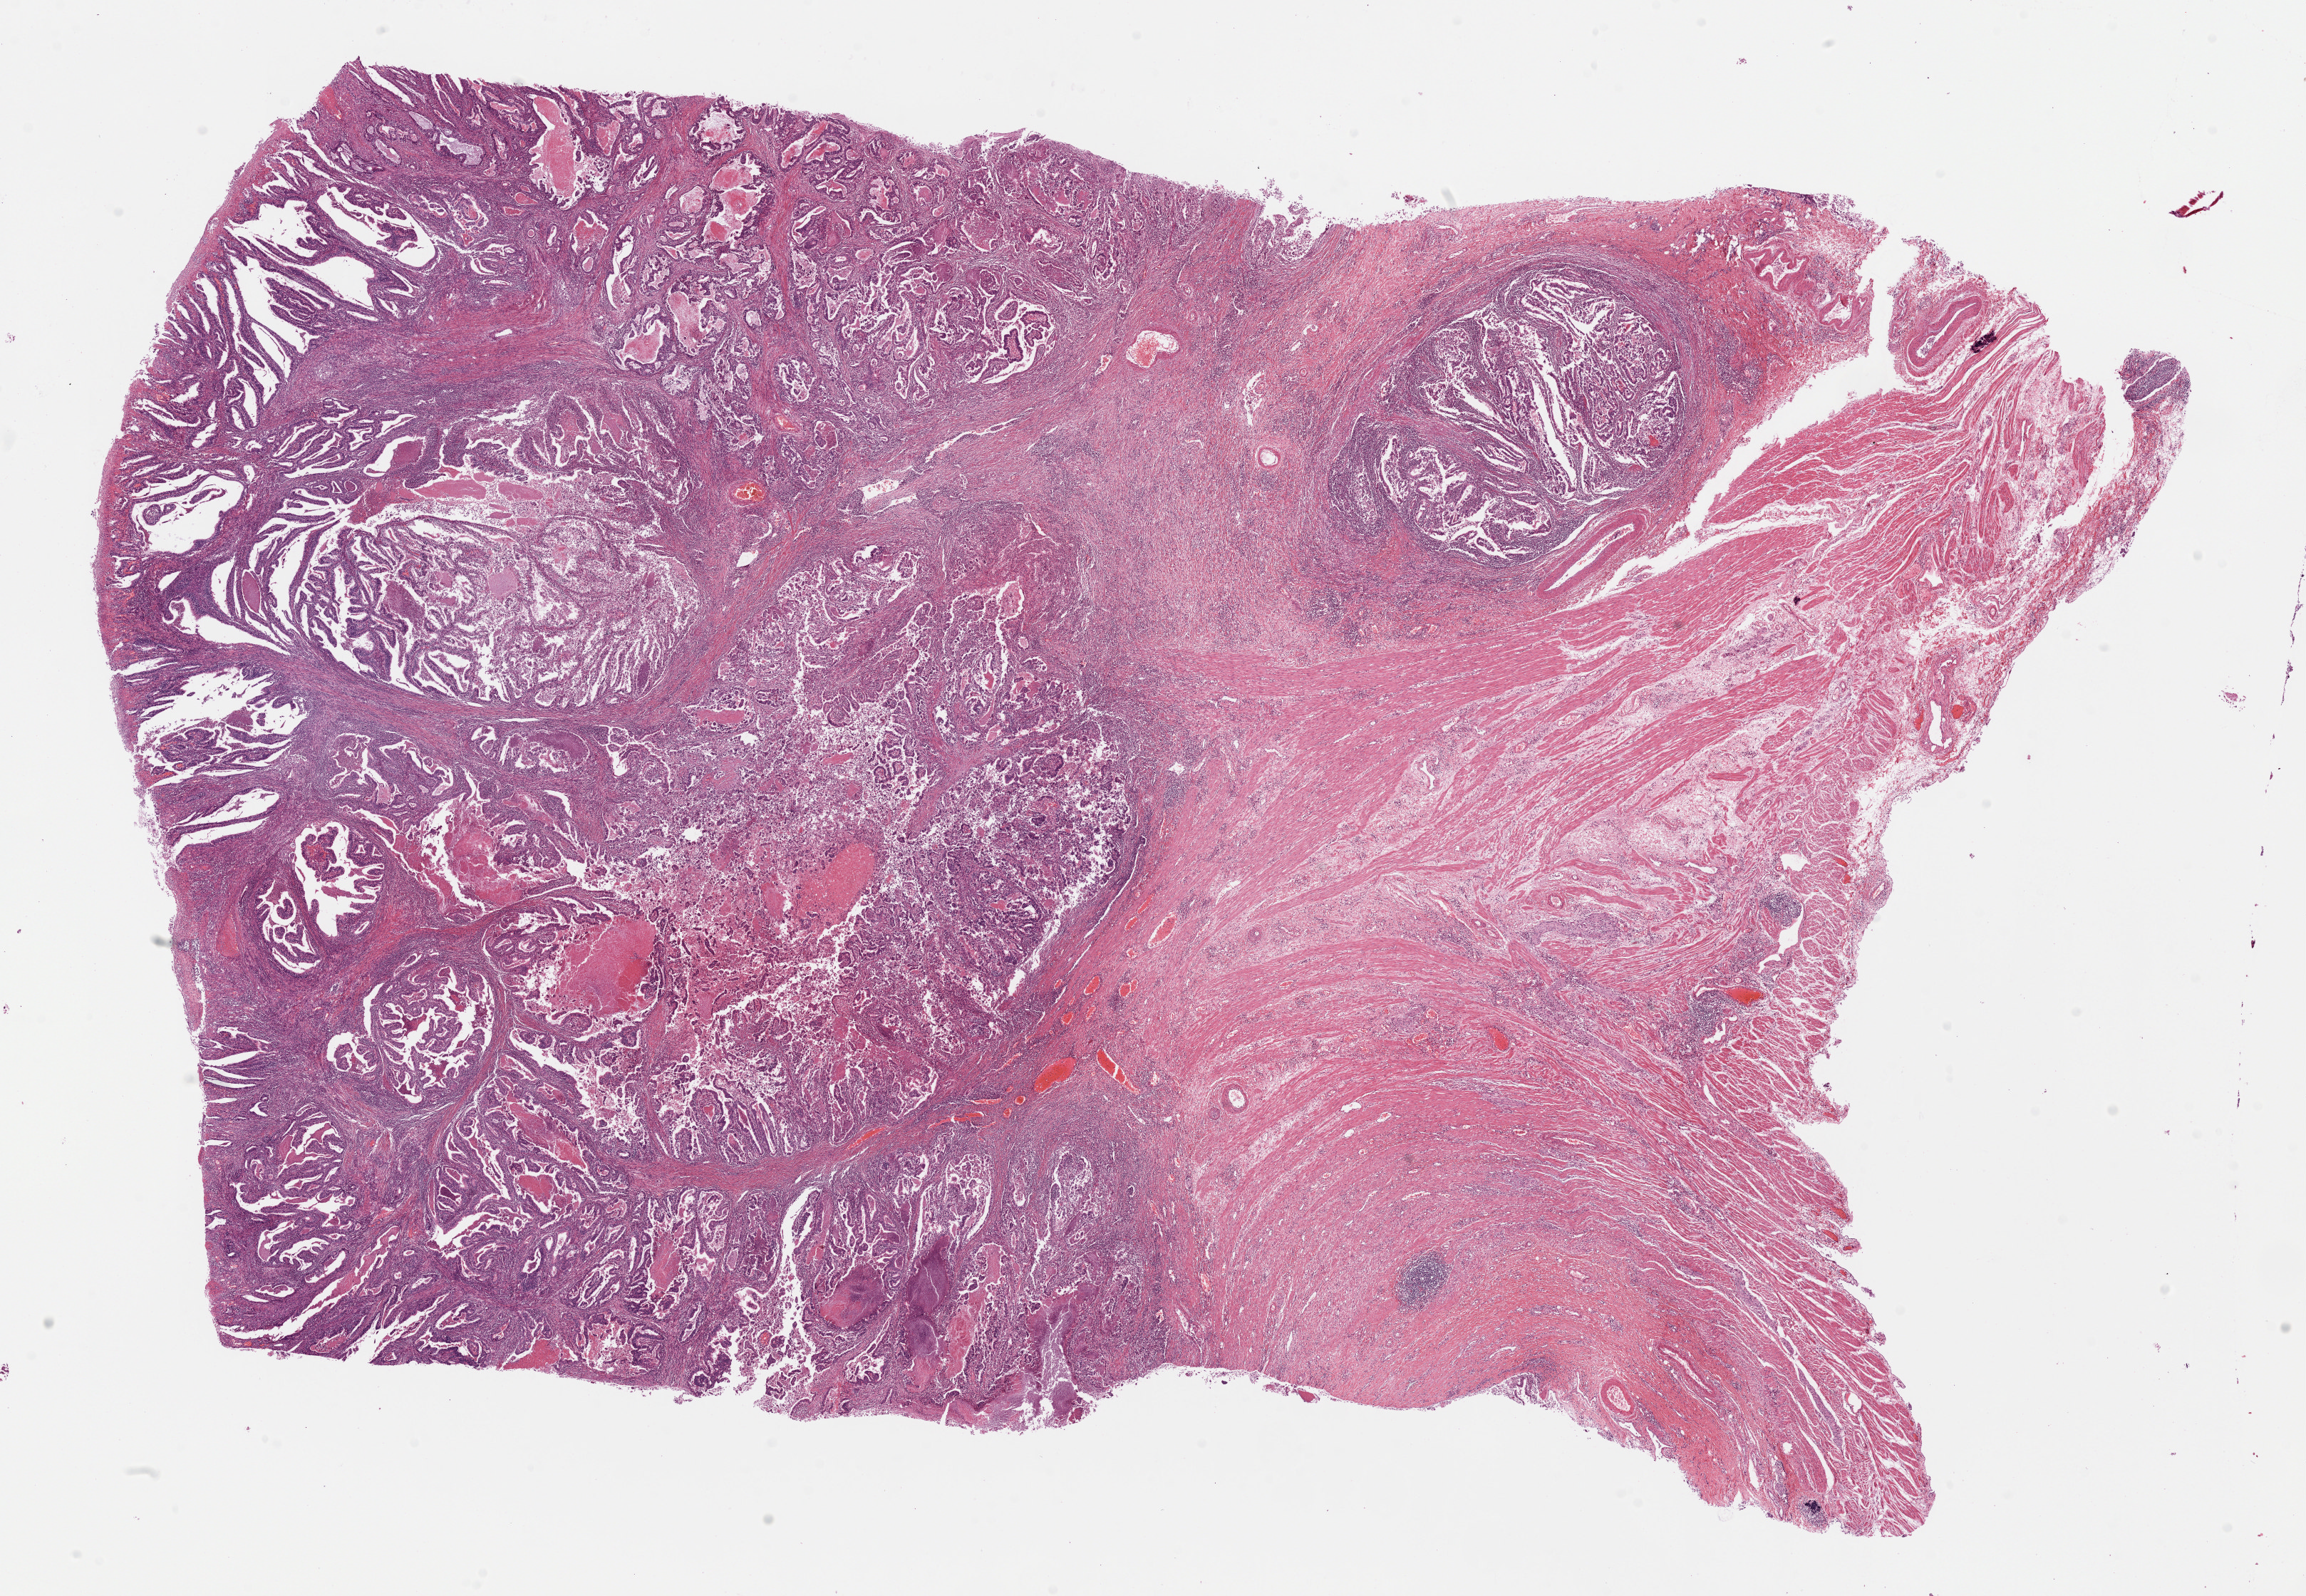
Whole-slide histology image, Hematoxylin and eosin (H&E) stained, a low-resolution overview of the entire scanned area, about 25.6 x 17.7 mm (from a 20x scan), FFPE section, stomach, primary tumour sample. Male, age 71 years at initial diagnosis. Histologic grade: GX (grade cannot be assessed).
AJCC pathologic stage: IB (7th edition). TNM: T2 N0 M0. Lymph nodes positive (case pathology): 0 of 73 examined. Pathologic diagnosis: Papillary adenocarcinoma, NOS (fundus of stomach).